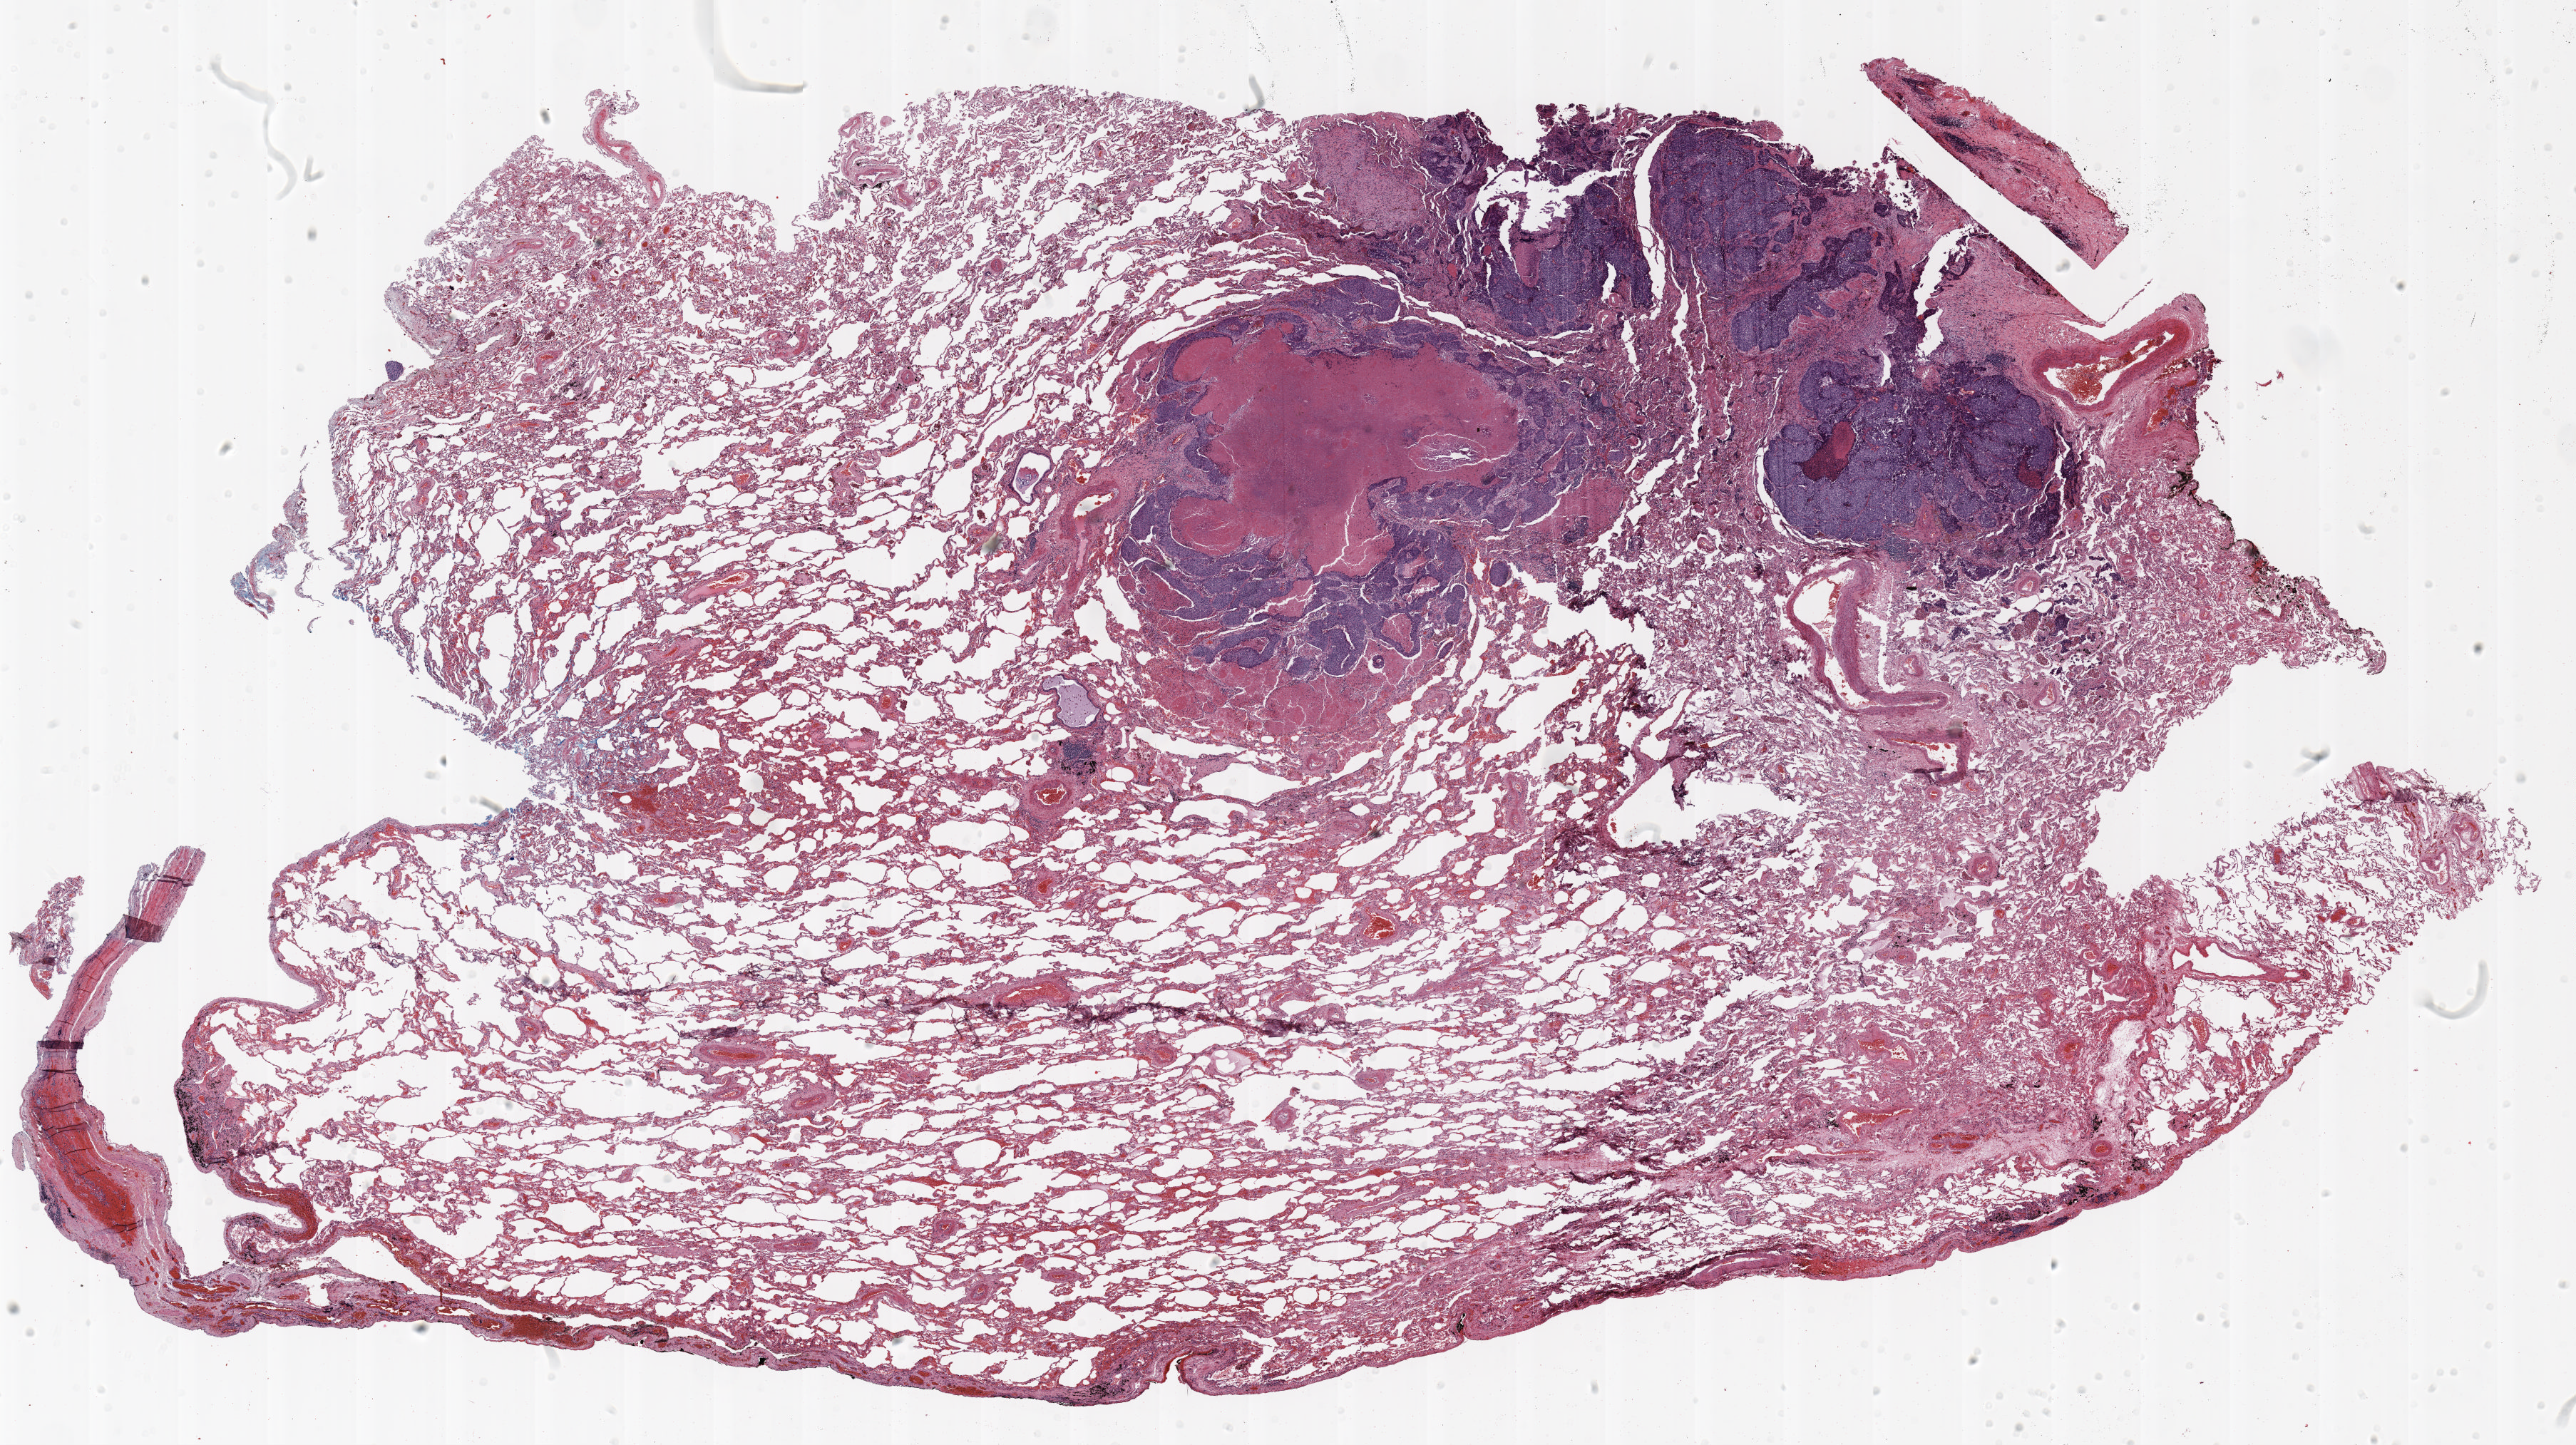
Whole-slide histology image, H&E-stained — low-resolution overview of the scanned area, about 29.0 x 16.3 mm; formalin-fixed paraffin-embedded (FFPE) section; lung tissue. Male patient, aged 65 at enrolment. Current smoker at enrolment. Grade: poorly differentiated (G3).
- participant's lung-cancer diagnosis: Squamous cell carcinoma, NOS
- stage (AJCC 6th edition): IA
- primary tumour location (clinical record): left upper lobe
- tumour size (pathology): 18 mm